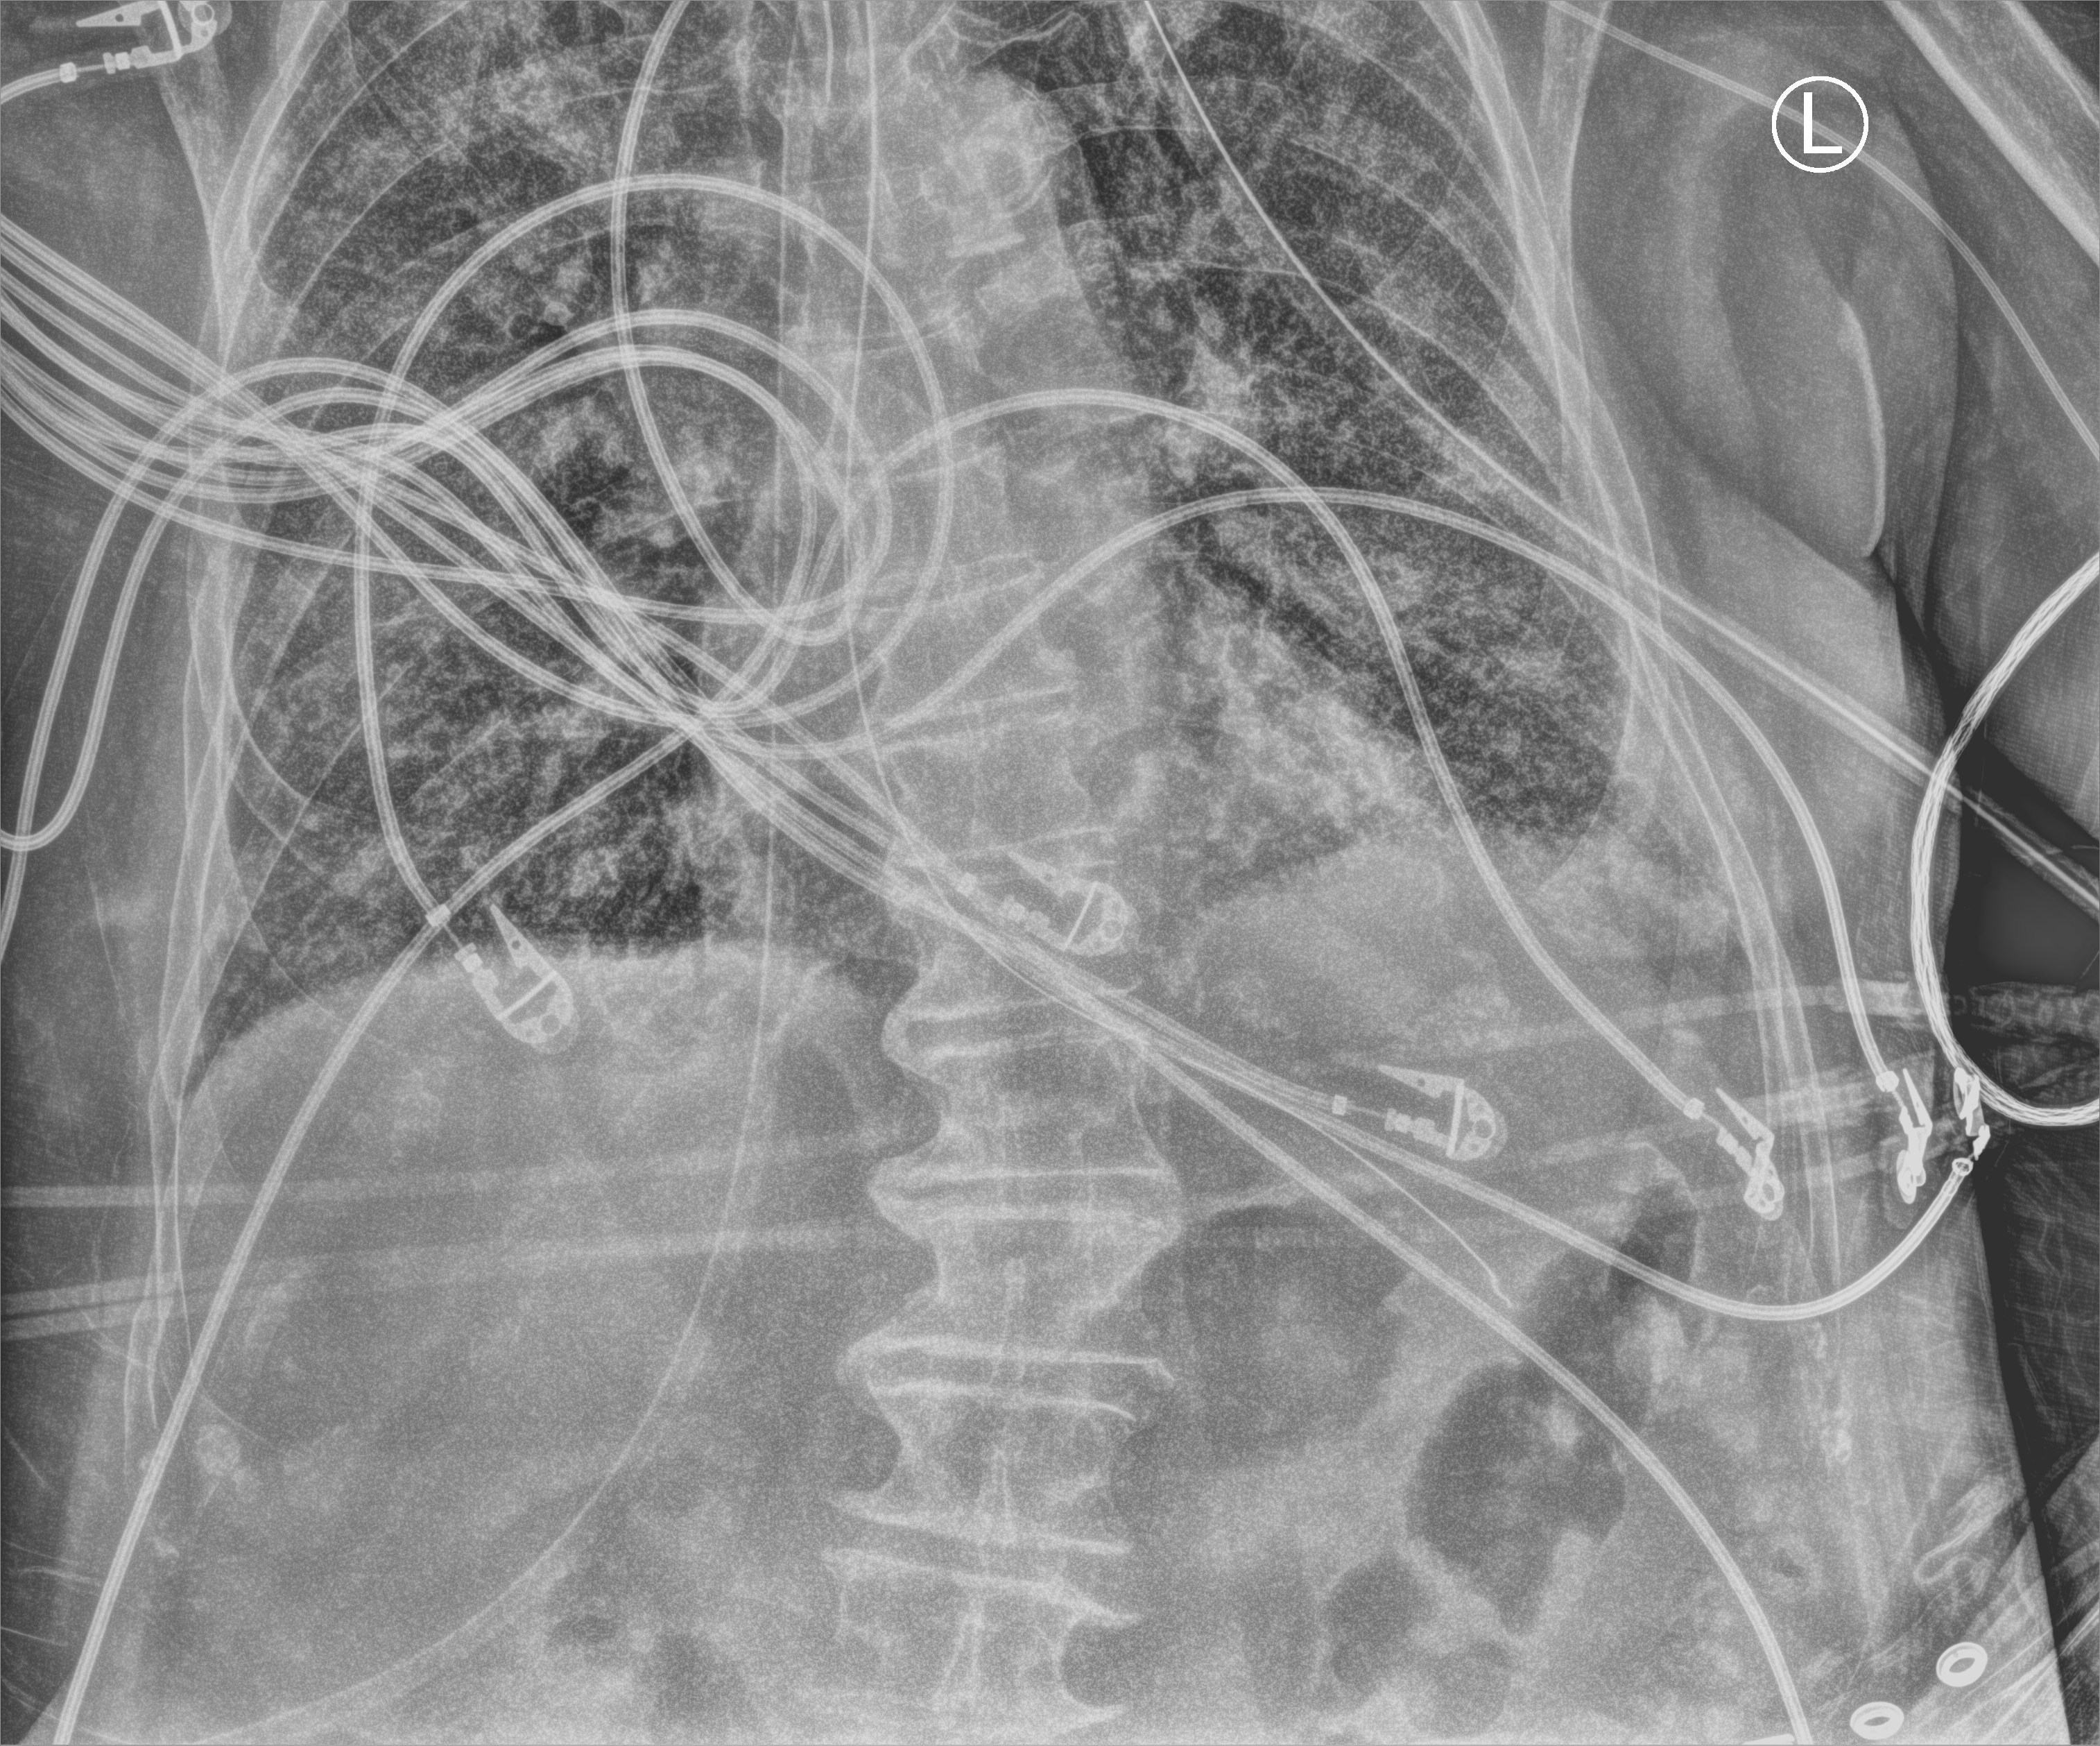
Chest X-ray (portable), anteroposterior (AP) projection. Male patient hospitalised with COVID-19, age 75–90 years.
Hospital-stay facts (about this admission, not read from this image; timing relative to this image not recorded): mechanically ventilated during this hospital stay: yes; chronic kidney disease (admission record): no; admitted to intensive care during this hospital stay: yes.